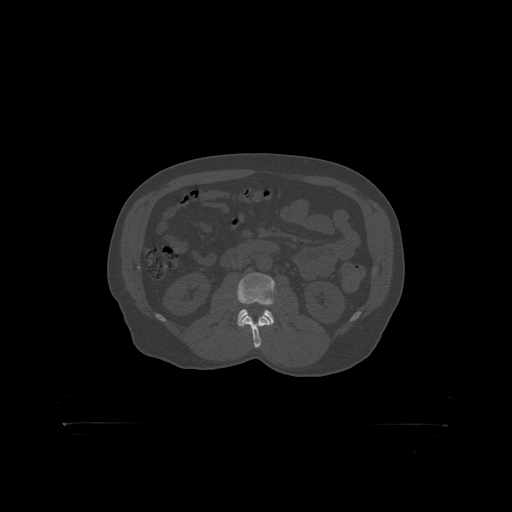
CT including the spine, one axial slice; slice 281 of 399 in the series (ordered by position); bone window (W 1800 / L 400 HU); 1.25 mm slice thickness; 512 × 512 image matrix, field of view 650 × 650 mm. Male patient, age 46 years. From the clinical record (not read from this slice): primary cancer: skin.
Annotated regions visible in this slice (semi-automatic segmentation, software-assisted and operator-edited):
- L2 vertebra: bounding box (x1, y1, x2, y2) in pixels: (243, 315, 266, 319)
- L3 vertebra: (238, 273, 276, 319)